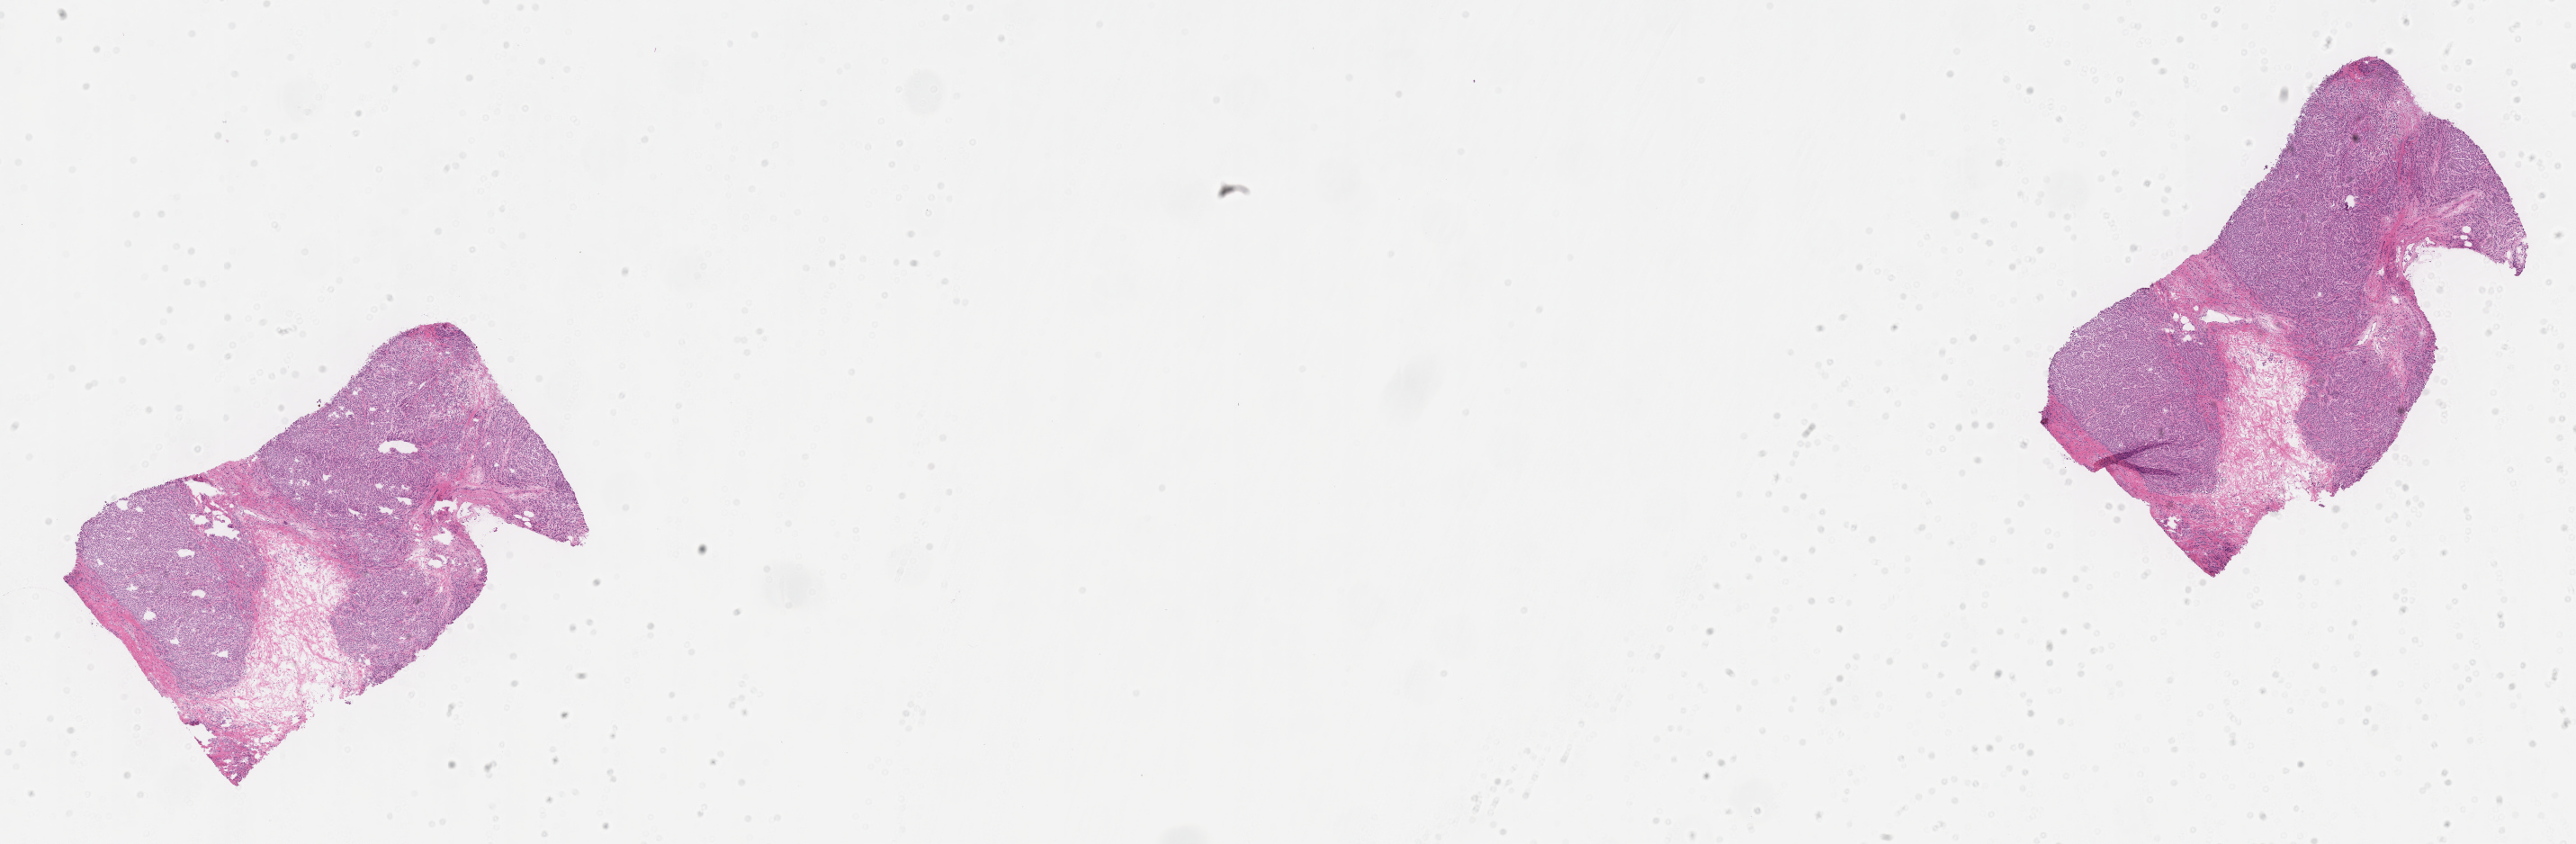
H&E whole-slide image — whole scanned area (about 23.1 x 7.6 mm) shown as a low-resolution overview, cryosection, primary tumor, anatomic site: breast. Female, age 83 years at initial diagnosis. Composition of this section per pathologist review: tumor cells 75%, tumor nuclei 75%, stromal cells 15%, necrosis 0%, normal cells 10%. Inflammatory infiltration, as recorded: lymphocyte infiltration 2%, monocyte infiltration 2%, neutrophil infiltration 0%.
Histologic diagnosis: Lobular carcinoma, NOS. Section: top of the tissue portion.